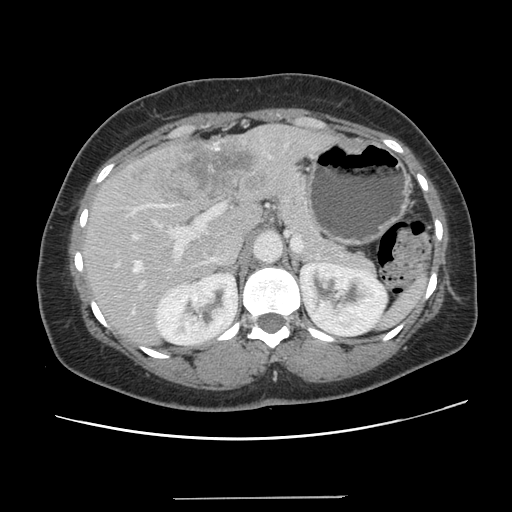
Contrast-enhanced abdominal CT, one axial slice. Position 81 of 141 along the scan axis. 120 kVp. Intravenous contrast given. Soft-tissue window (W 400 / L 40 HU). 2.5 mm slice thickness. 512 × 512 image matrix. Female patient, age 53 years. Case-level facts recorded for this patient, not image findings: diagnosis: colorectal cancer liver metastases, imaged before liver resection; multiple liver metastases: no; largest metastasis: 14.5 cm; disease in both lobes: yes.
Structures marked on this image (expert manual segmentation):
- hepatic veins: bounding box [x1, y1, x2, y2] px = [133, 207, 141, 272]
- liver: [83, 126, 334, 344]
- planned liver remnant (the part of the liver to remain after resection): [84, 206, 262, 345]
- portal vein (with intrahepatic branches): [132, 204, 223, 291]
- liver metastasis: [133, 138, 271, 204]